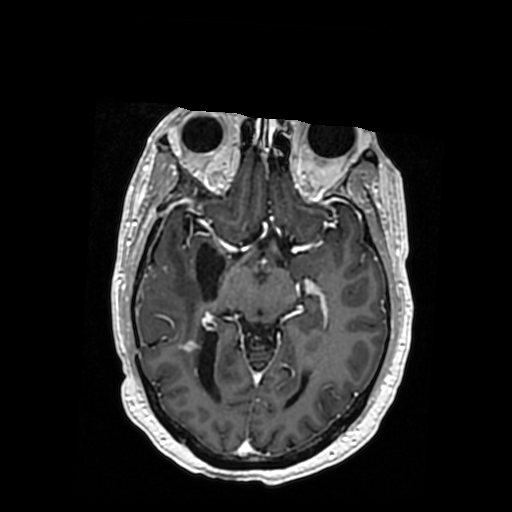
Brain MRI from a brain-tumour surgery series, one axial slice. Position 204 of 364 along the scan axis. T1-weighted post-contrast. 0.5 mm slice thickness. 512 × 512 image matrix, field of view 260 × 260 mm. From the clinical record (not read from this slice): histopathology: Oligodendroglioma; WHO grade: 3; IDH mutation: yes.
Structures marked on this image (manually delineated by an expert):
- previous resection cavity: bounding box [x1, y1, x2, y2] px = [196, 243, 225, 300]
- tumour: [157, 336, 172, 346]